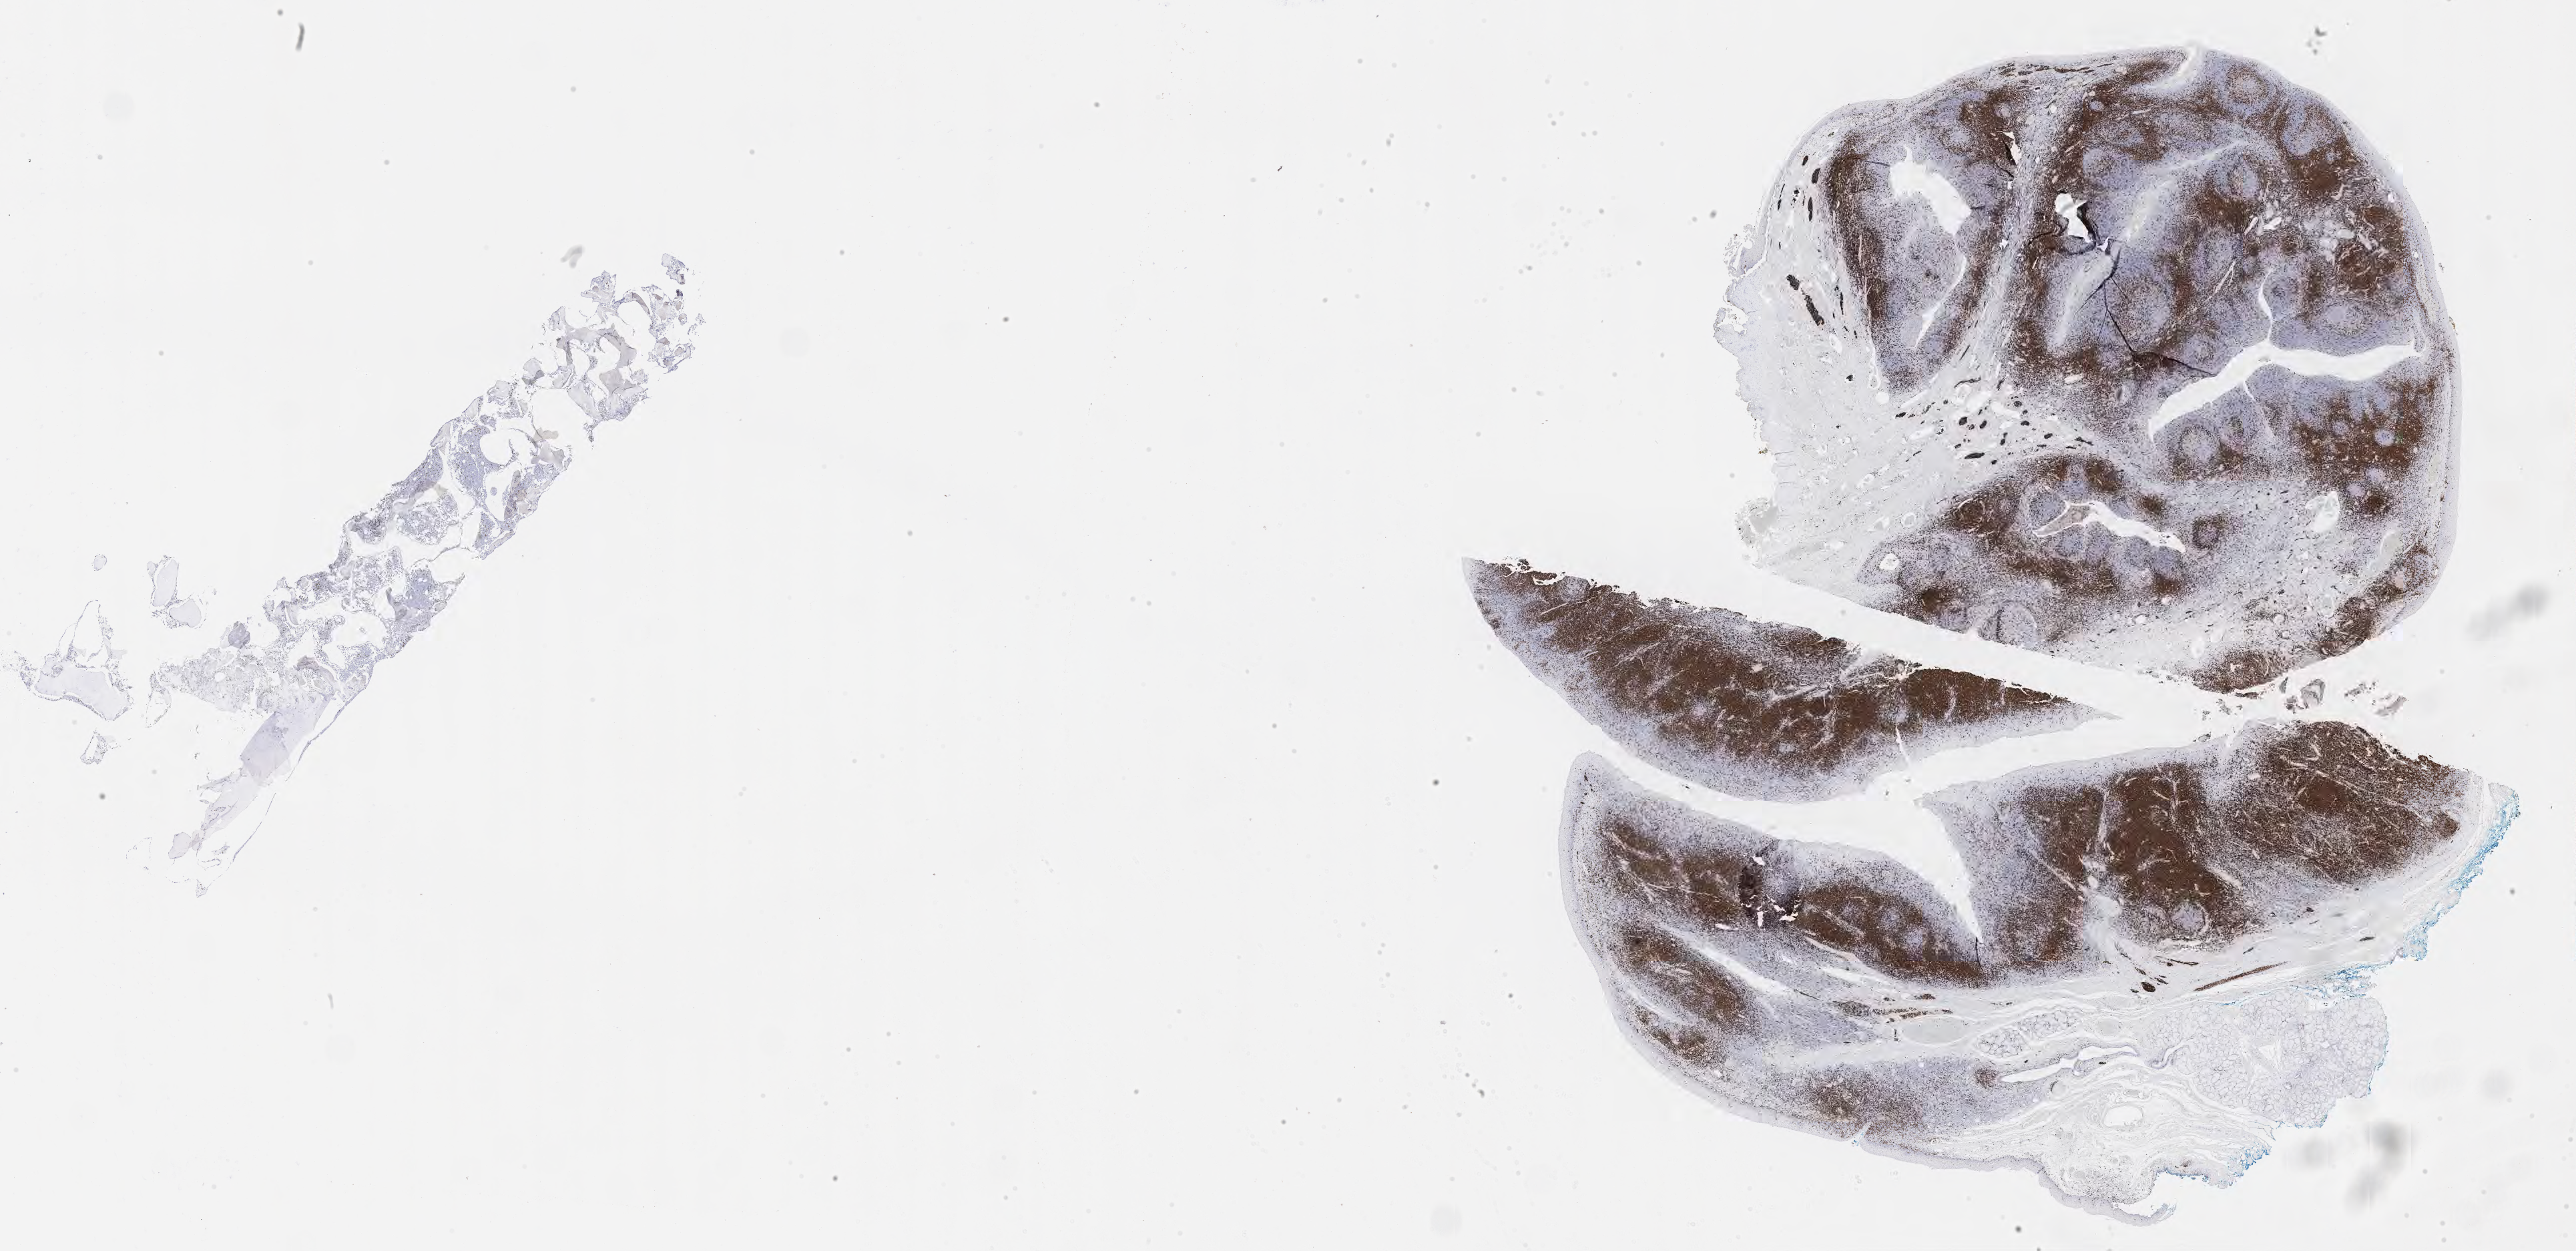
IHC for CD3, whole-slide image, shown as a low-resolution overview of the whole scanned area (about 31.2 x 15.1 mm); specimen: tumor tissue. Patient: male, age 13 years.
Diagnosis: Burkitt lymphoma, NOS.